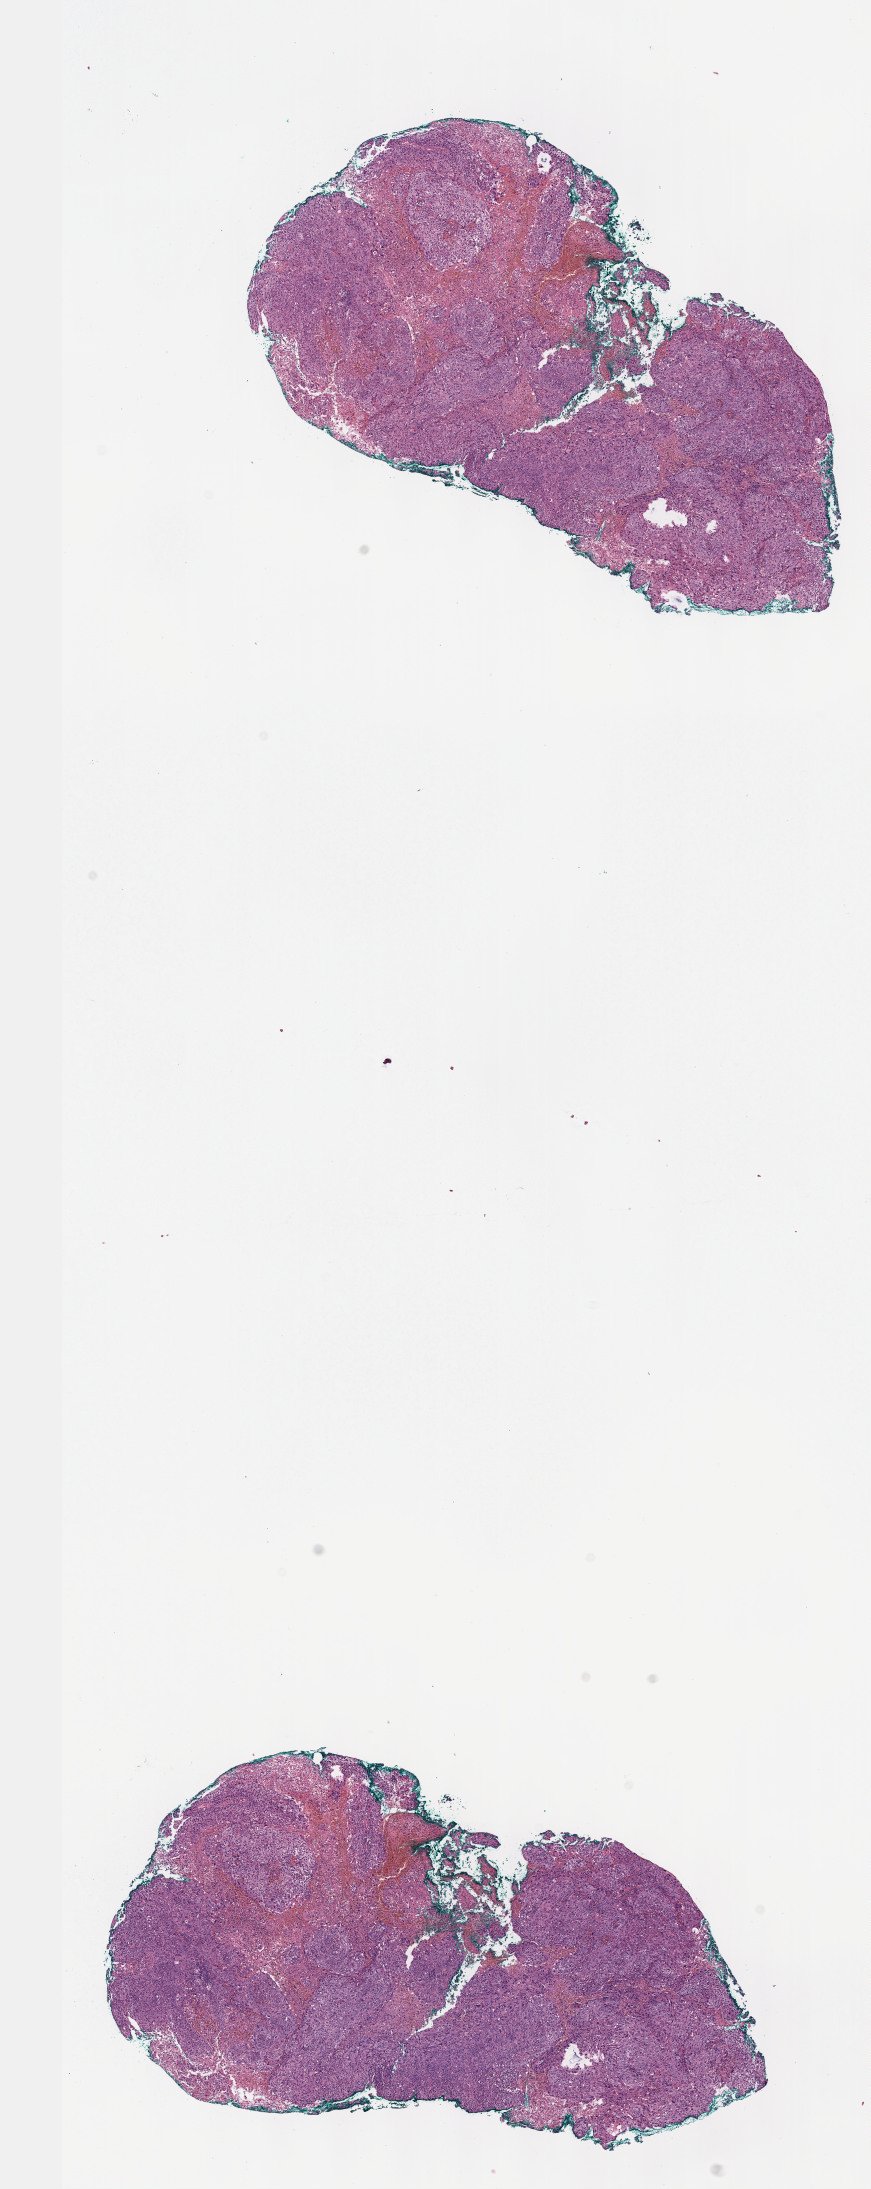
Whole-slide histology image, H&E-stained, low-resolution overview of the scanned area, about 7.0 x 17.7 mm (from a 40x scan); FFPE section; cervix, primary tumour sample. Female, age 38 years at initial diagnosis.
Diagnosis: Squamous cell carcinoma, NOS.